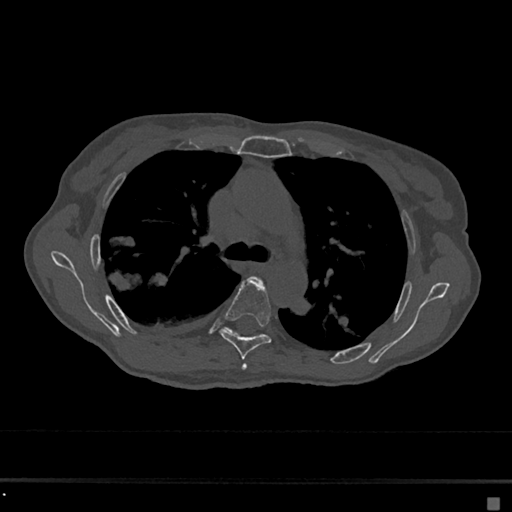
CT including the spine, one axial slice. Slice 459 of 797 in the series (ordered by position). Reconstruction kernel Br40s/3. Bone window (W 1800 / L 400 HU). 0.5 mm slice thickness. 512 × 512 image matrix, field of view 360 × 360 mm. Patient: female, 68 years. From the clinical record (not read from this slice): primary cancer: renal.
Structures marked on this image (semi-automatic segmentation, software-assisted and operator-edited):
- T4 vertebra: bounding box [x1, y1, x2, y2] px = [242, 276, 264, 370]
- T5 vertebra: [220, 279, 272, 360]
- T6 vertebra: [226, 328, 261, 336]